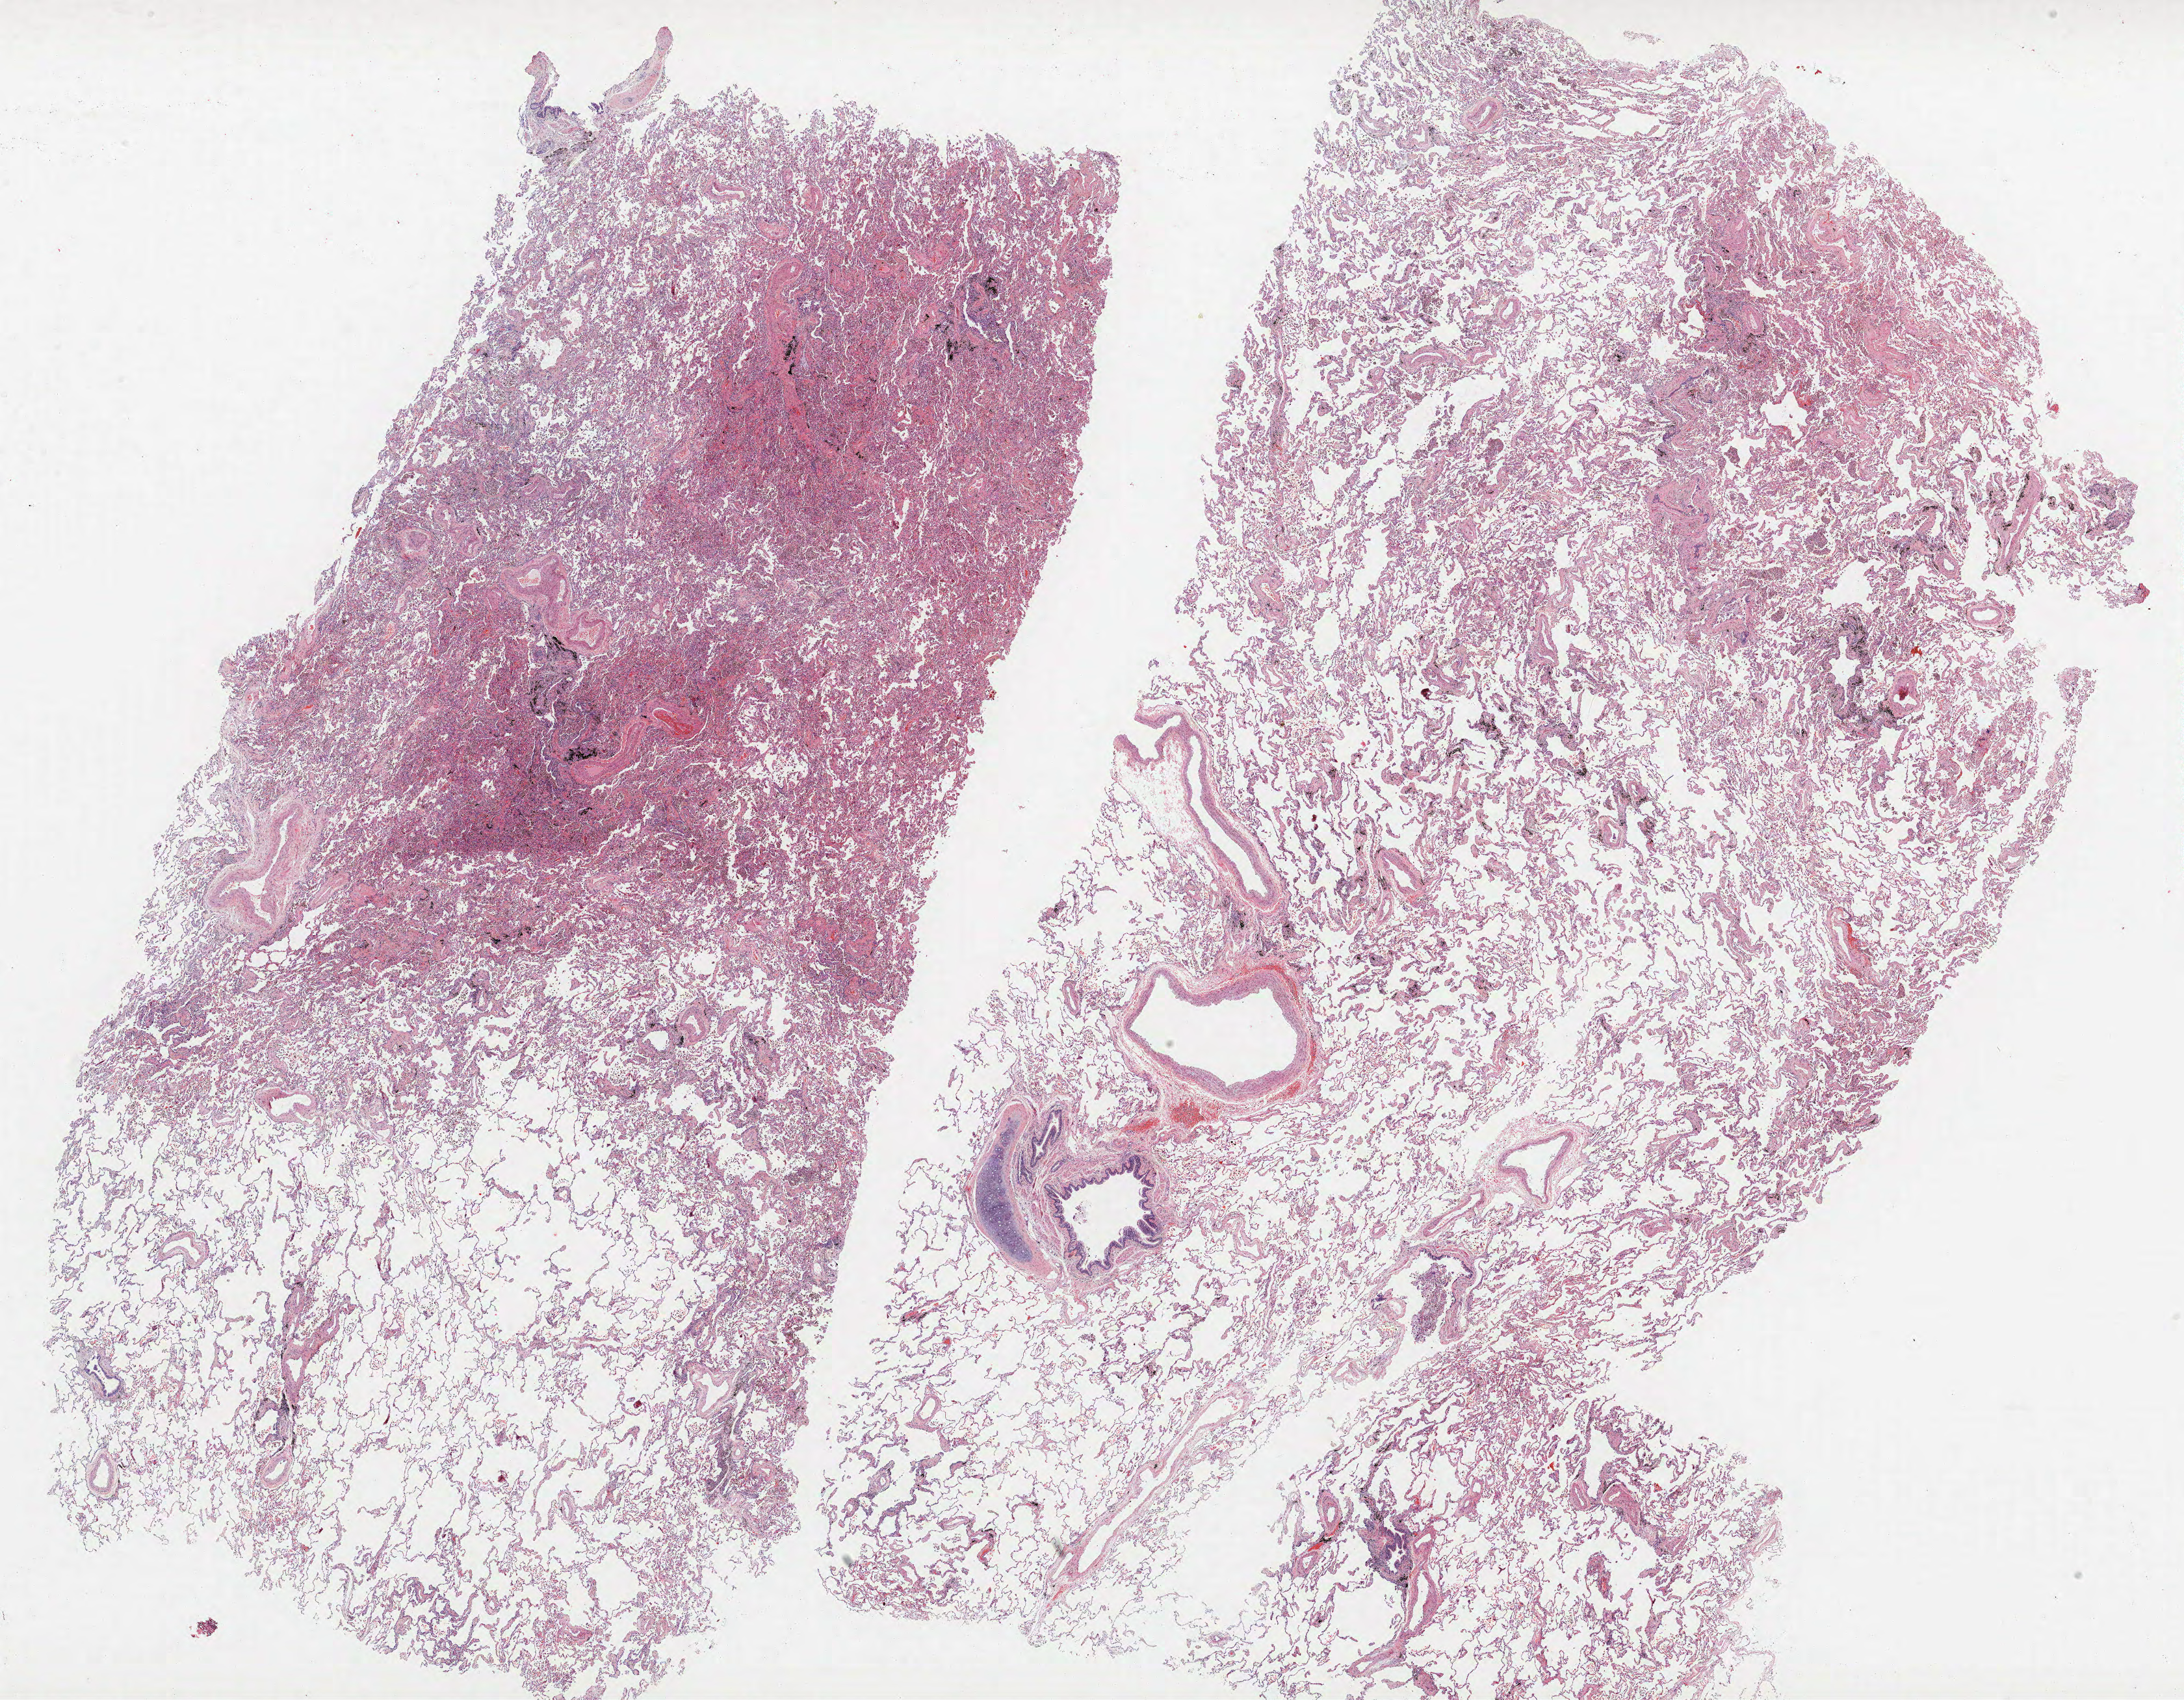
Hematoxylin and eosin (H&E) stained whole-slide image, a low-resolution overview of the entire scanned area, about 26.9 x 20.9 mm (from a 40x scan); FFPE section; lung. Female, age 66 at enrolment. Current smoker at enrolment. Grade: poorly differentiated (G3).
Tumour size (pathology): 14 mm. Participant's lung-cancer diagnosis: Squamous cell carcinoma, keratinizing, NOS (ICD-O-3 8071/3). Primary tumour location (clinical record): right upper lobe, right middle lobe. Stage (AJCC 6th edition): IA. ICD-O-3 topography: overlapping lesion of lung (C34.8).